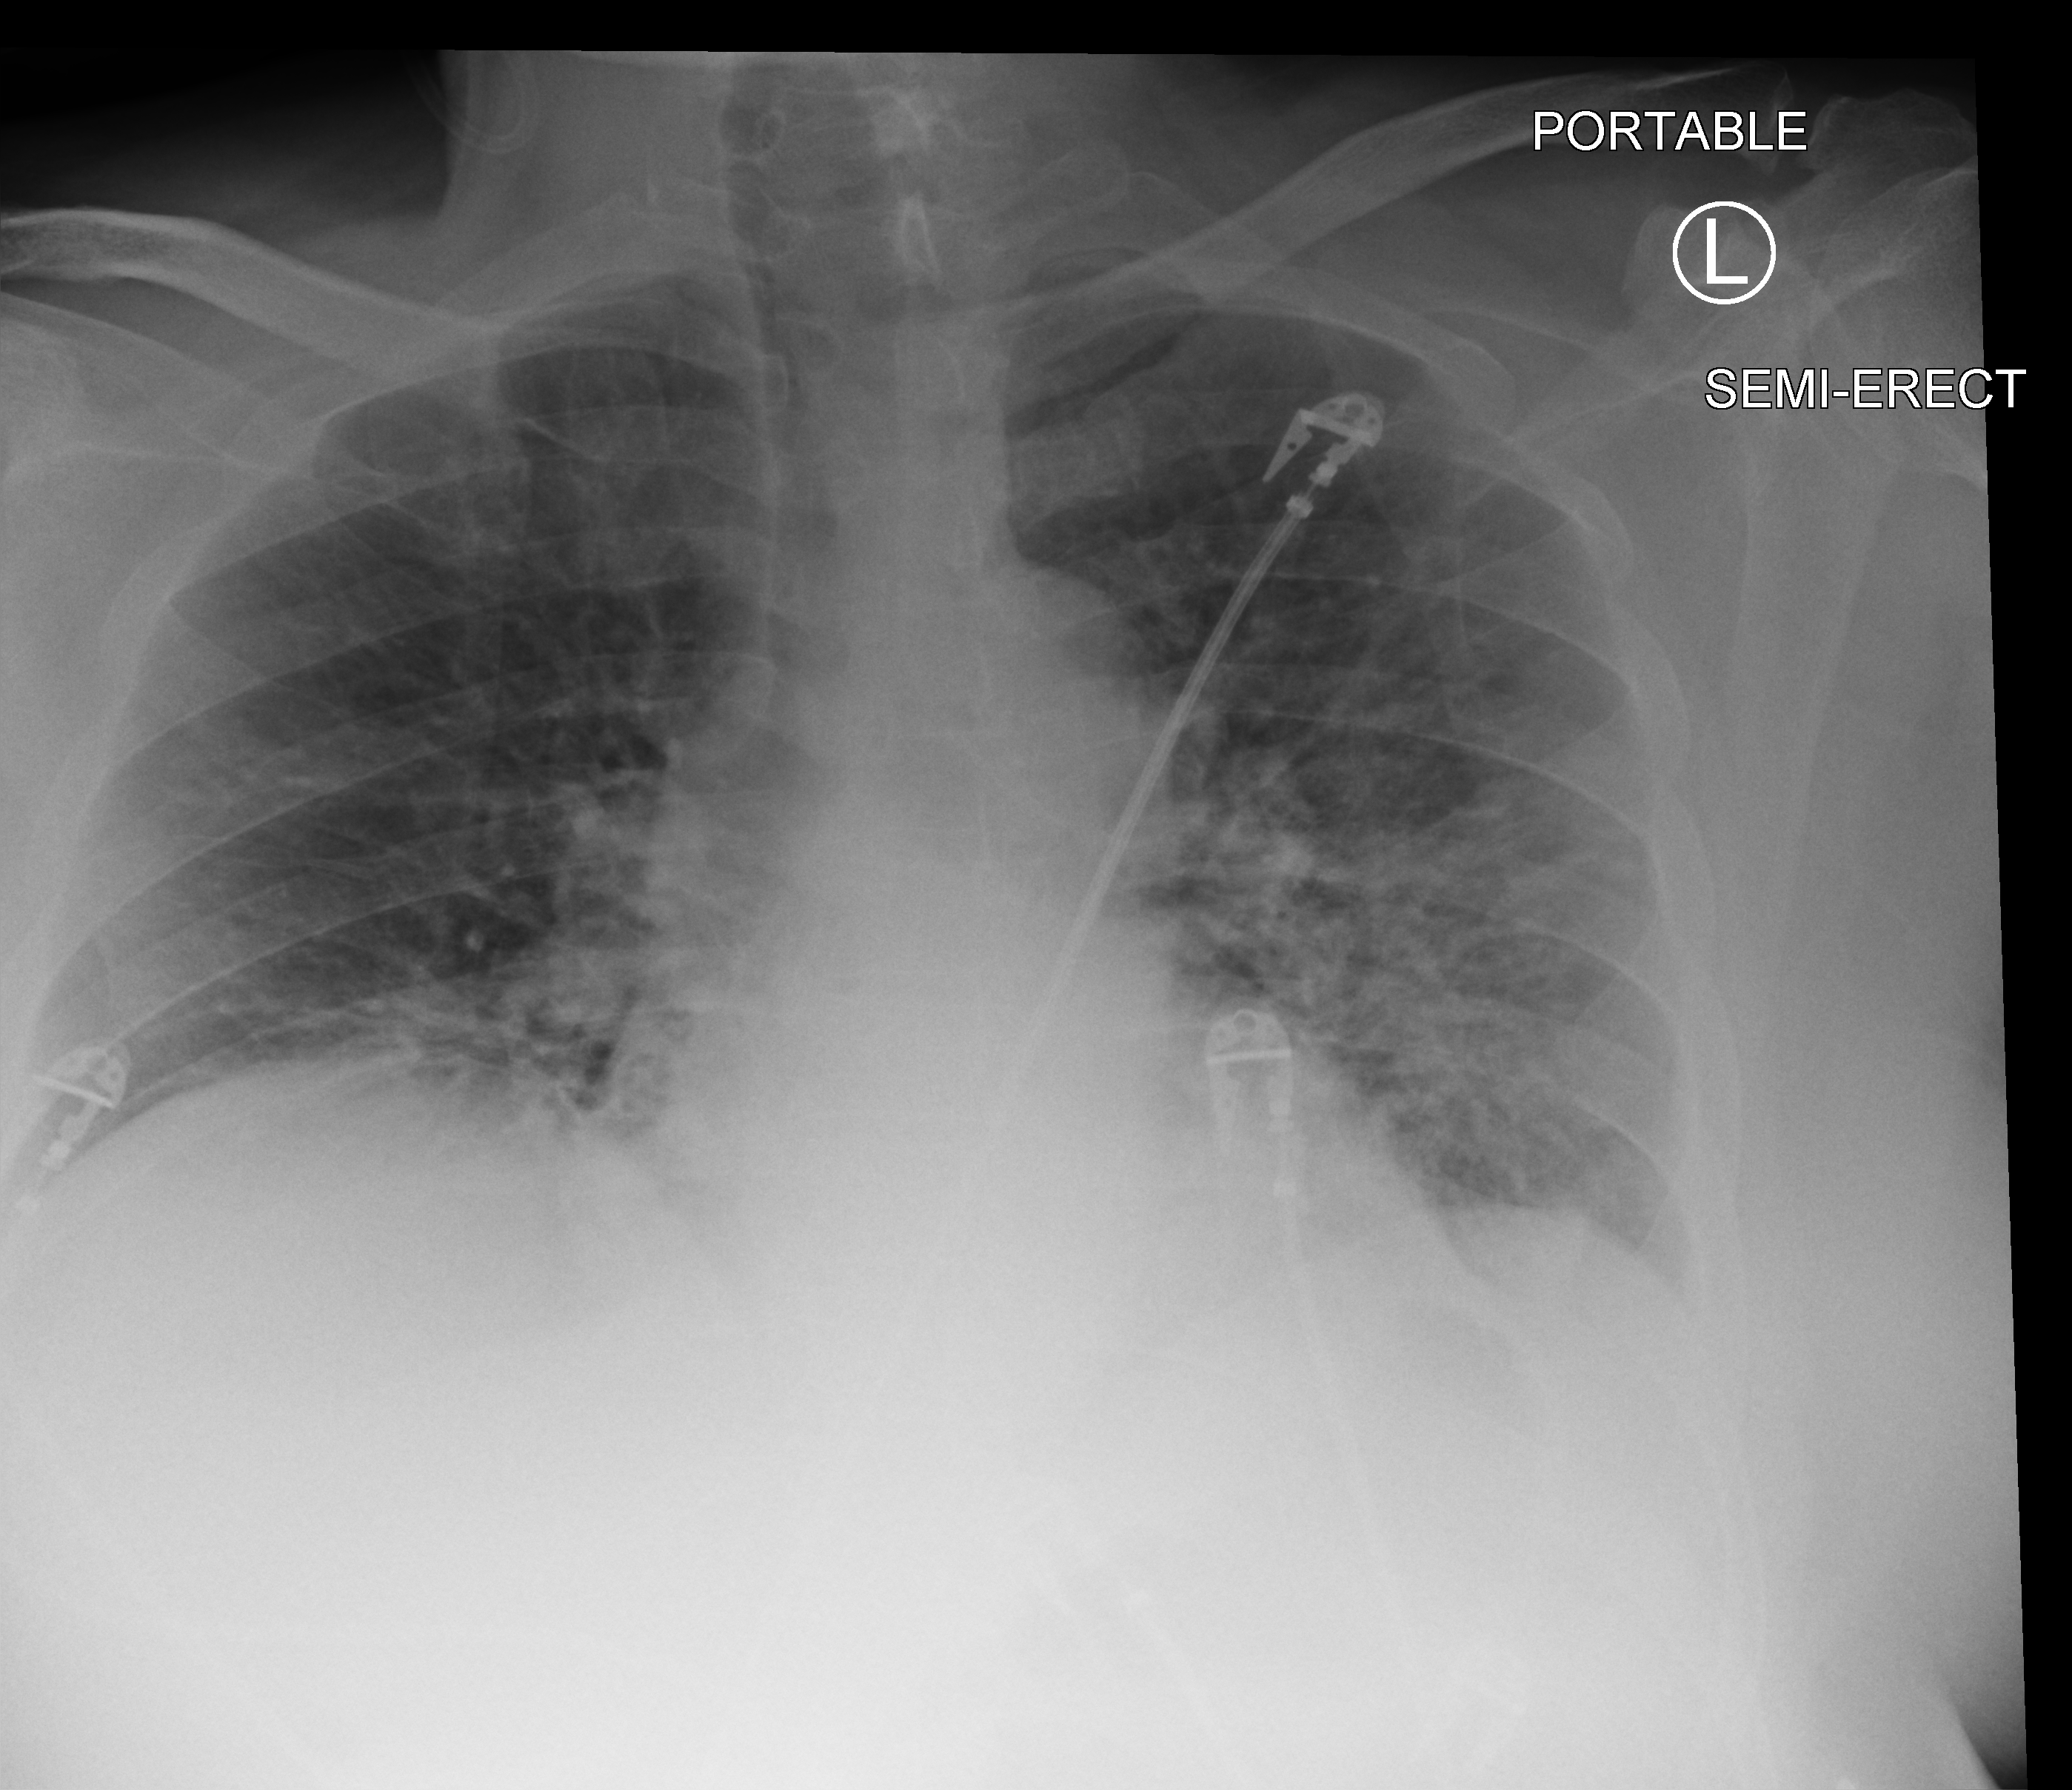
Bedside chest radiograph (computed radiography), anteroposterior (AP) projection. Male patient hospitalised with COVID-19, age 18–59 years.
Admission-level facts for this patient (not findings on this image; timing relative to this image not recorded): admitted to intensive care during this hospital stay: no.